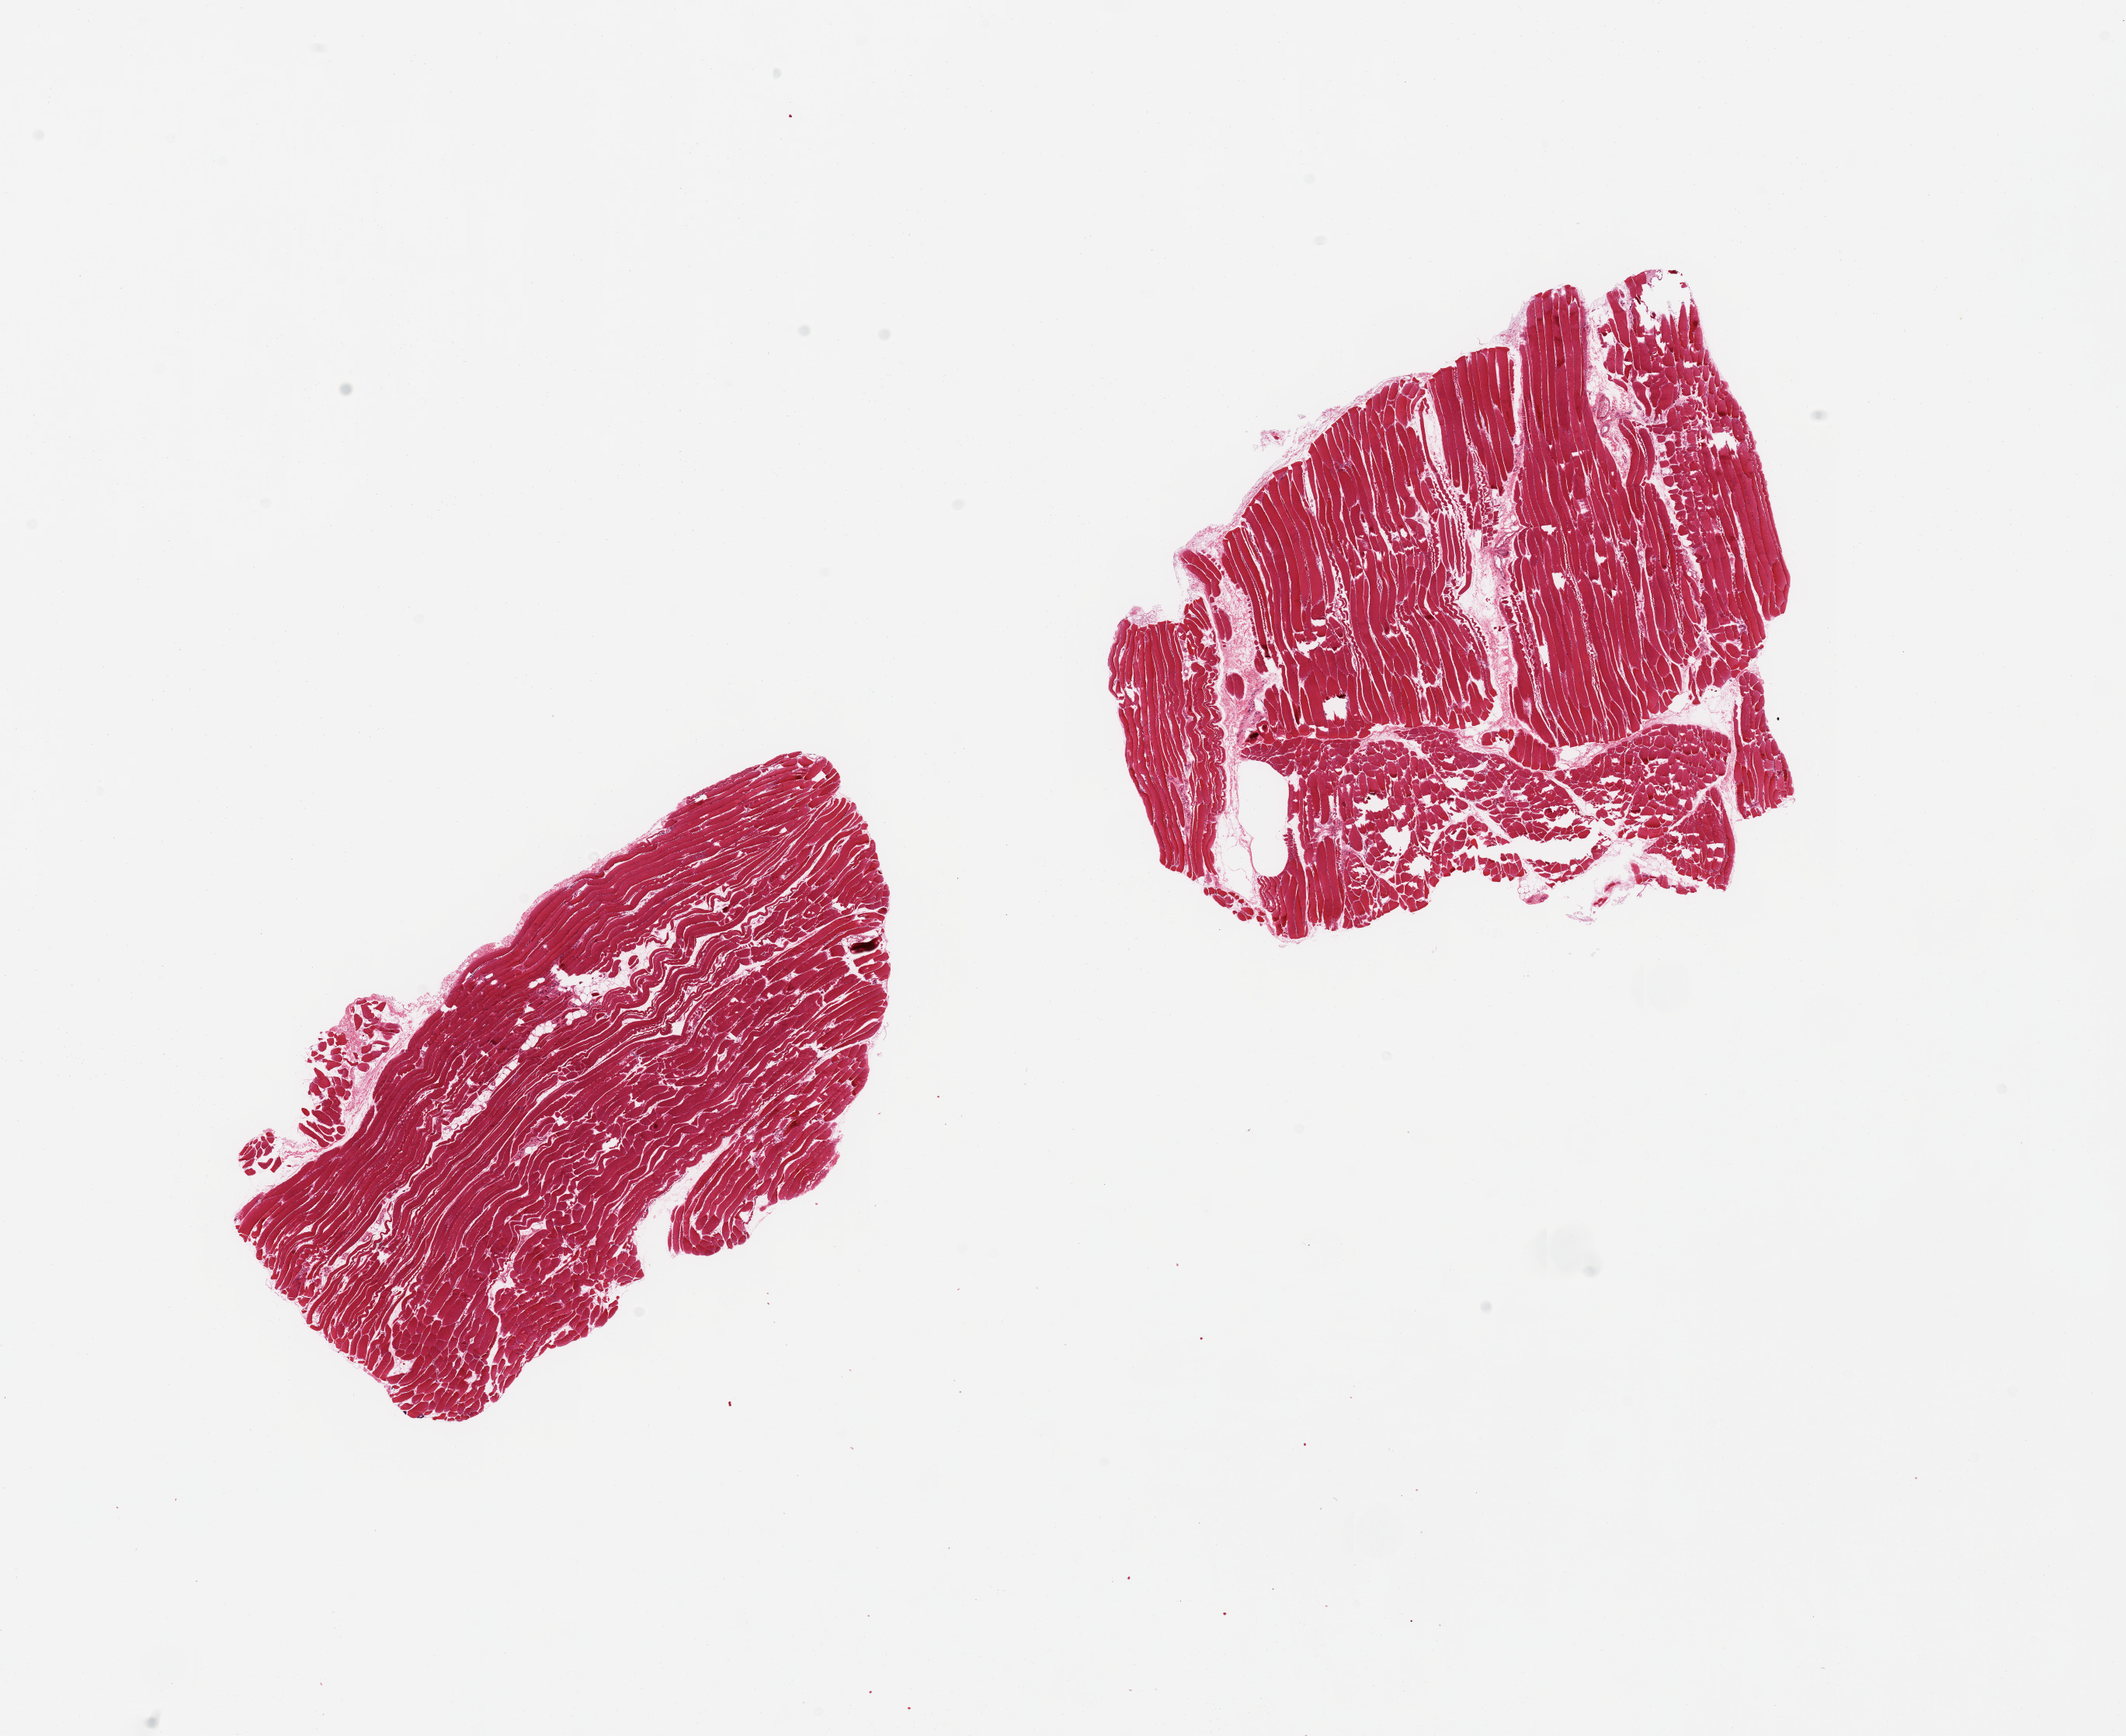
Whole-slide image, hematoxylin and eosin (H&E) stain, brightfield — low-resolution overview of the scanned area, about 21.7 x 17.7 mm, PAXgene-fixed, paraffin-embedded tissue, target tissue: skeletal muscle, tissue donor sample. Female donor.
Review note (as recorded): 2 pieces, scattered atrophic fibers.